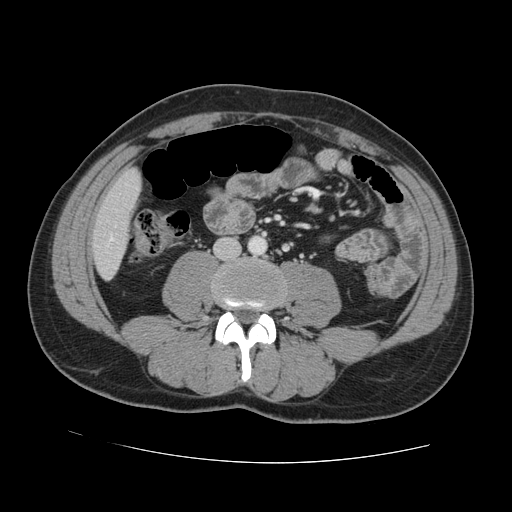
Contrast-enhanced abdominal CT, one axial slice; slice 20 of 131 in the series (ordered by position); 120 kVp; intravenous contrast given; soft-tissue window (W 400 / L 40 HU); 2.5 mm slice thickness; 512 × 512 image matrix, field of view 380 × 380 mm. Male patient, age 40 years. From the clinical record (not read from this slice): diagnosis: colorectal cancer liver metastases, imaged before liver resection; multiple liver metastases: yes; largest metastasis: 2.9 cm; disease in both lobes: yes.
Structures marked on this image (expert manual segmentation):
- hepatic veins: bounding box (x1, y1, x2, y2) in pixels: (110, 237, 113, 241)
- liver: (93, 171, 140, 277)